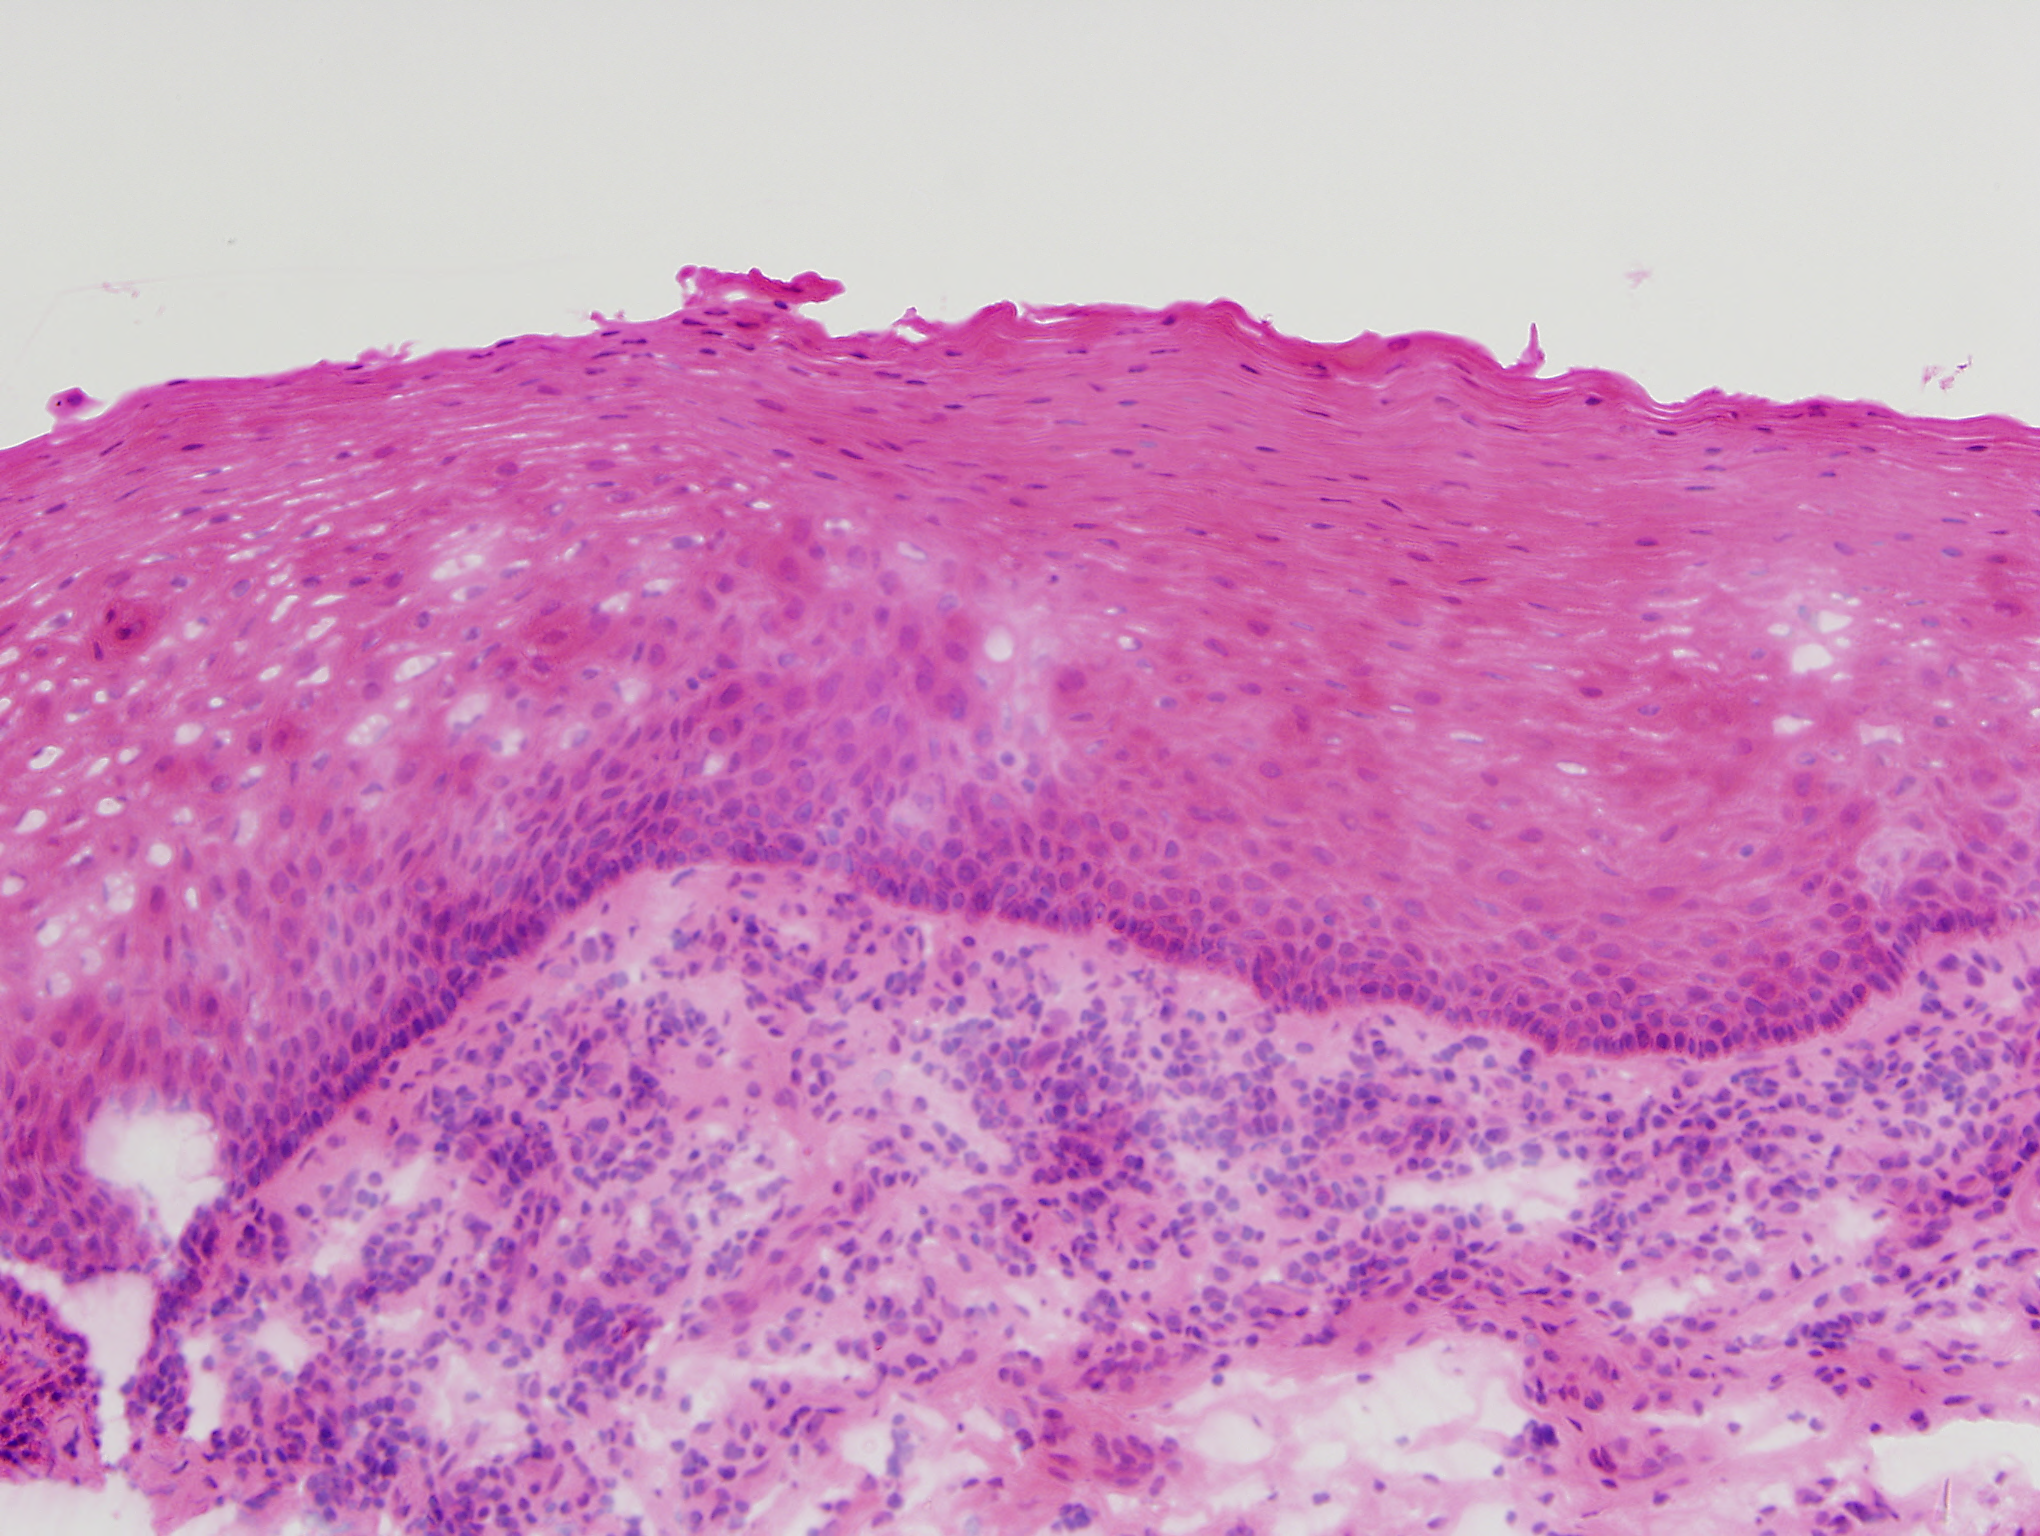
H&E-stained image of one small field of the section, about 1.0 x 0.8 mm across, frozen section from the top of the tissue portion, solid tissue normal (non-tumour tissue) sample from the head and neck. Male, age 67 years at initial diagnosis.
This section: solid tissue normal sample (biorepository sample class). Patient diagnosis: Squamous cell carcinoma, NOS (larynx, NOS).